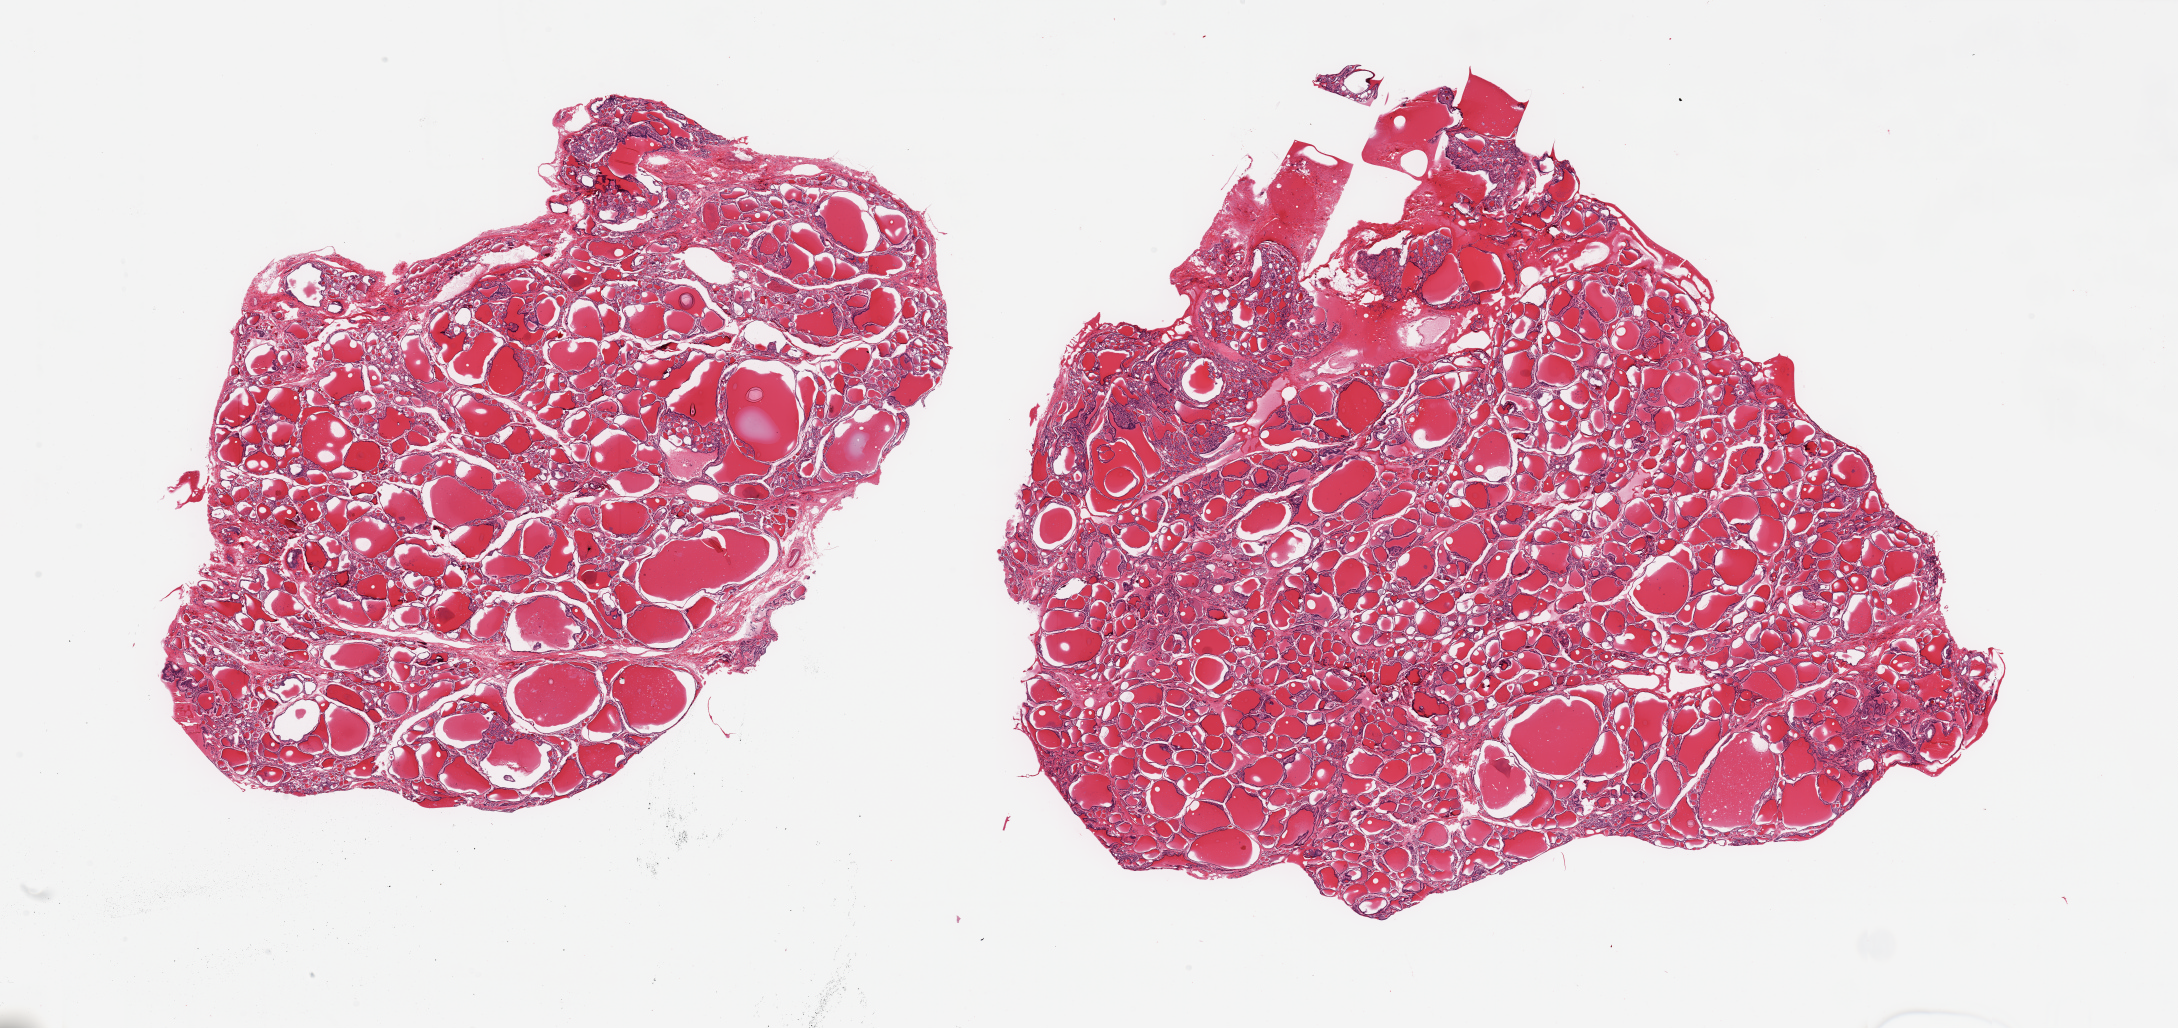
Digitized H&E-stained section, brightfield — whole scanned area (about 34.5 x 16.3 mm) shown as a low-resolution overview; PAXgene-fixed, paraffin-embedded tissue; target tissue: thyroid; tissue donor sample. Donor sex: male.
Reviewer comment on this tissue sample: 2 pieces, mulitple micro-colloid cysts, otherwise no abnormalities.